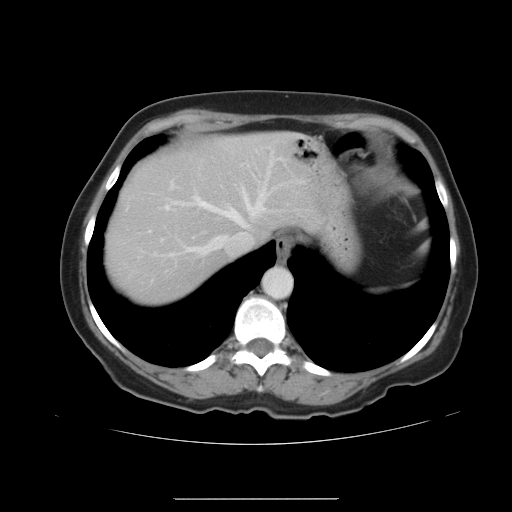
Contrast-enhanced abdominal CT, one axial slice; slice 32 of 41 in the series (ordered by position); intravenous contrast given; soft-tissue window (W 400 / L 40 HU); 512 × 512 image matrix. Female patient, age 63 years. From the clinical record (not read from this slice): diagnosis: colorectal cancer liver metastases, imaged before liver resection; multiple liver metastases: yes; largest metastasis: 1.5 cm; chemotherapy before resection: no.
Annotated regions visible in this slice (manually delineated by an expert):
- hepatic veins: bounding box (x1, y1, x2, y2) in pixels: (190, 147, 283, 252)
- liver: (105, 133, 312, 307)
- planned liver remnant (the part of the liver to remain after resection): (104, 133, 313, 307)